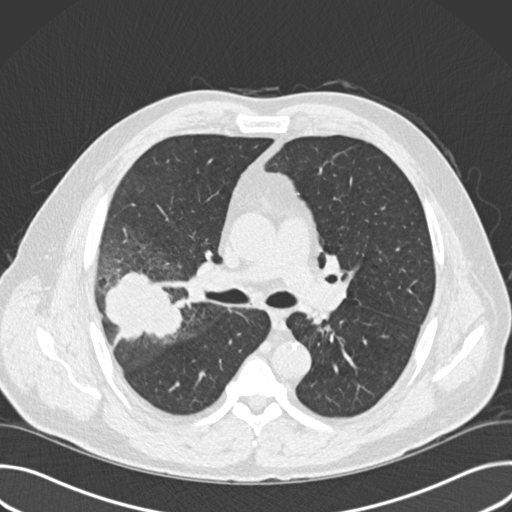
Low-dose screening chest CT, one axial slice; position 99 of 157 along the scan axis; lung window (W 1500 / L -600 HU); 2 mm slice thickness; 512 × 512 image matrix.
Outlined on this slice (expert manual segmentation):
- lesion 1 (tumor, upper lobe of right lung): bounding box [x1, y1, x2, y2] px = [105, 272, 183, 342]